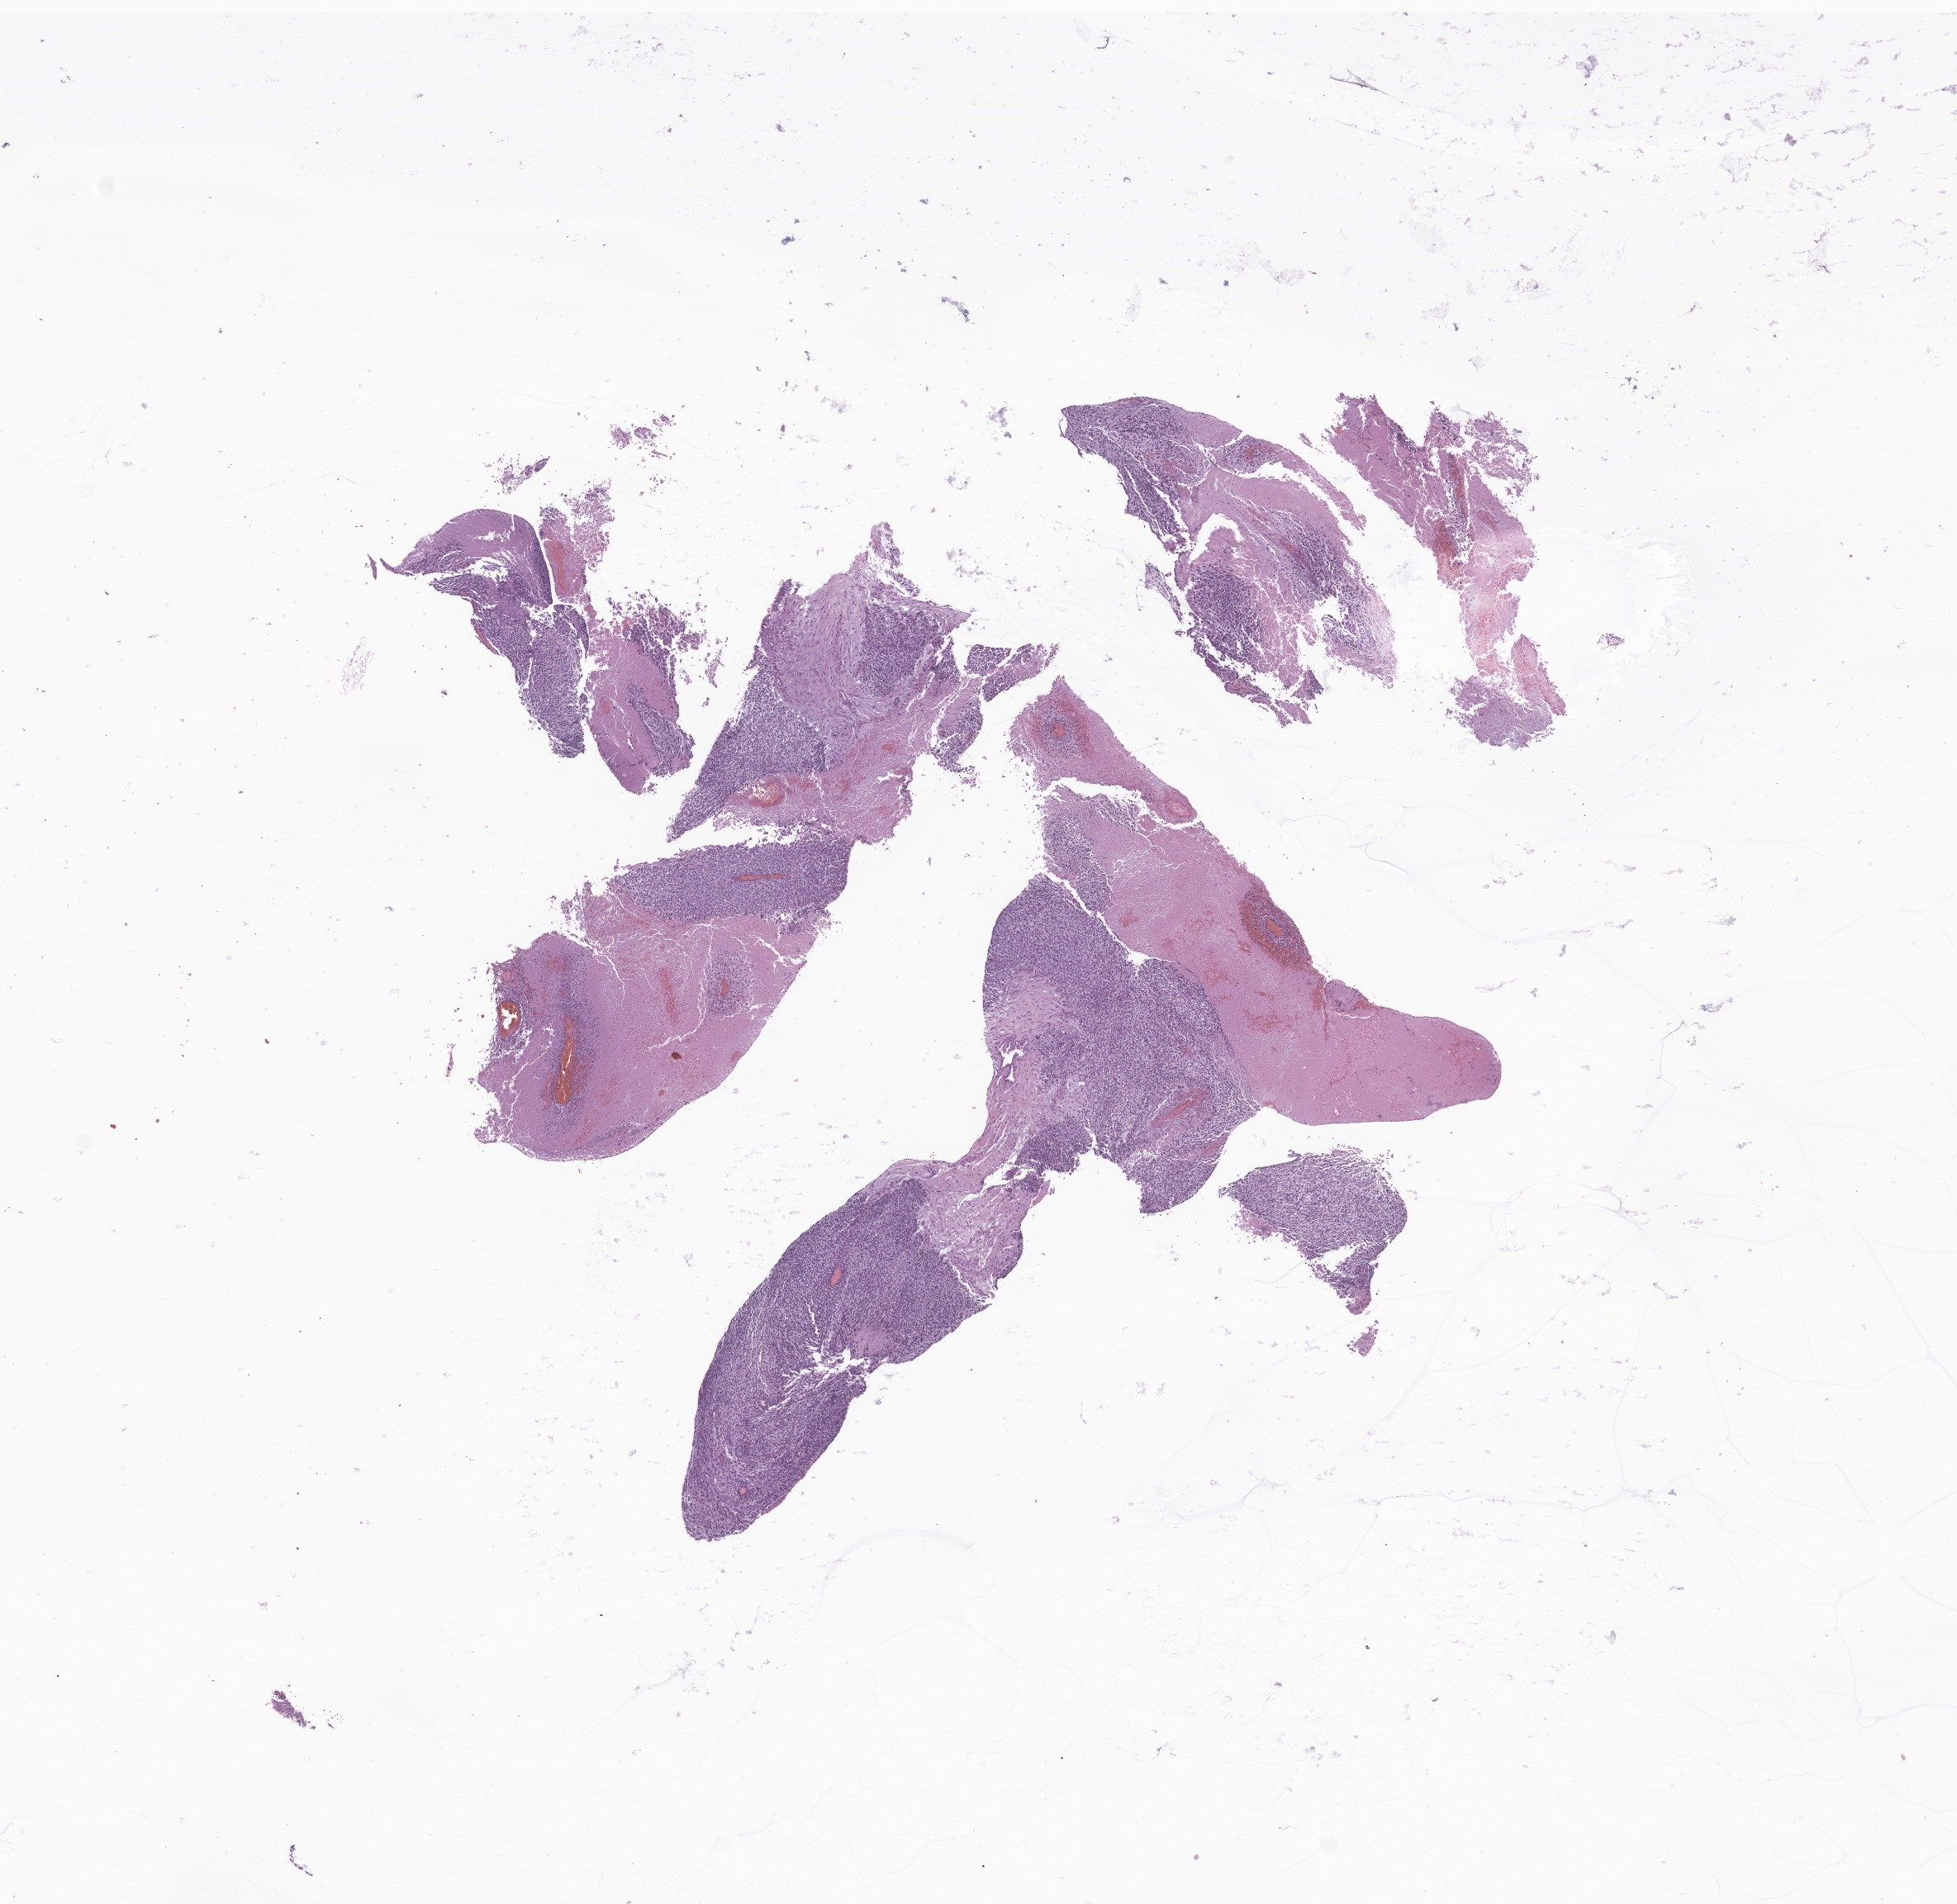
Digitized hematoxylin and eosin (H&E)-stained section of tumor tissue from the soft tissue — whole scanned area (about 10.0 x 9.7 mm) shown as a low-resolution overview. FFPE section. Patient: male, age 163 months.
Recorded diagnosis: Small cell sarcoma.